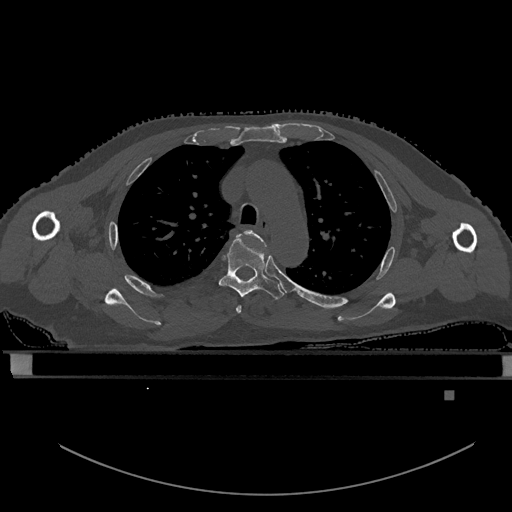
CT including the spine, one axial slice; position 412 of 969 along the scan axis; bone window (W 1800 / L 400 HU); 0.5 mm slice thickness; 512 × 512 image matrix, field of view 456 × 456 mm. Patient: male, 82 years. Case-level facts recorded for this patient, not image findings: primary cancer: prostate.
Structures marked on this image (semi-automatically segmented with operator editing):
- T3 vertebra: box from (x=236, y=230) to (x=268, y=313) px
- T4 vertebra: (x=219, y=237)–(x=284, y=299)